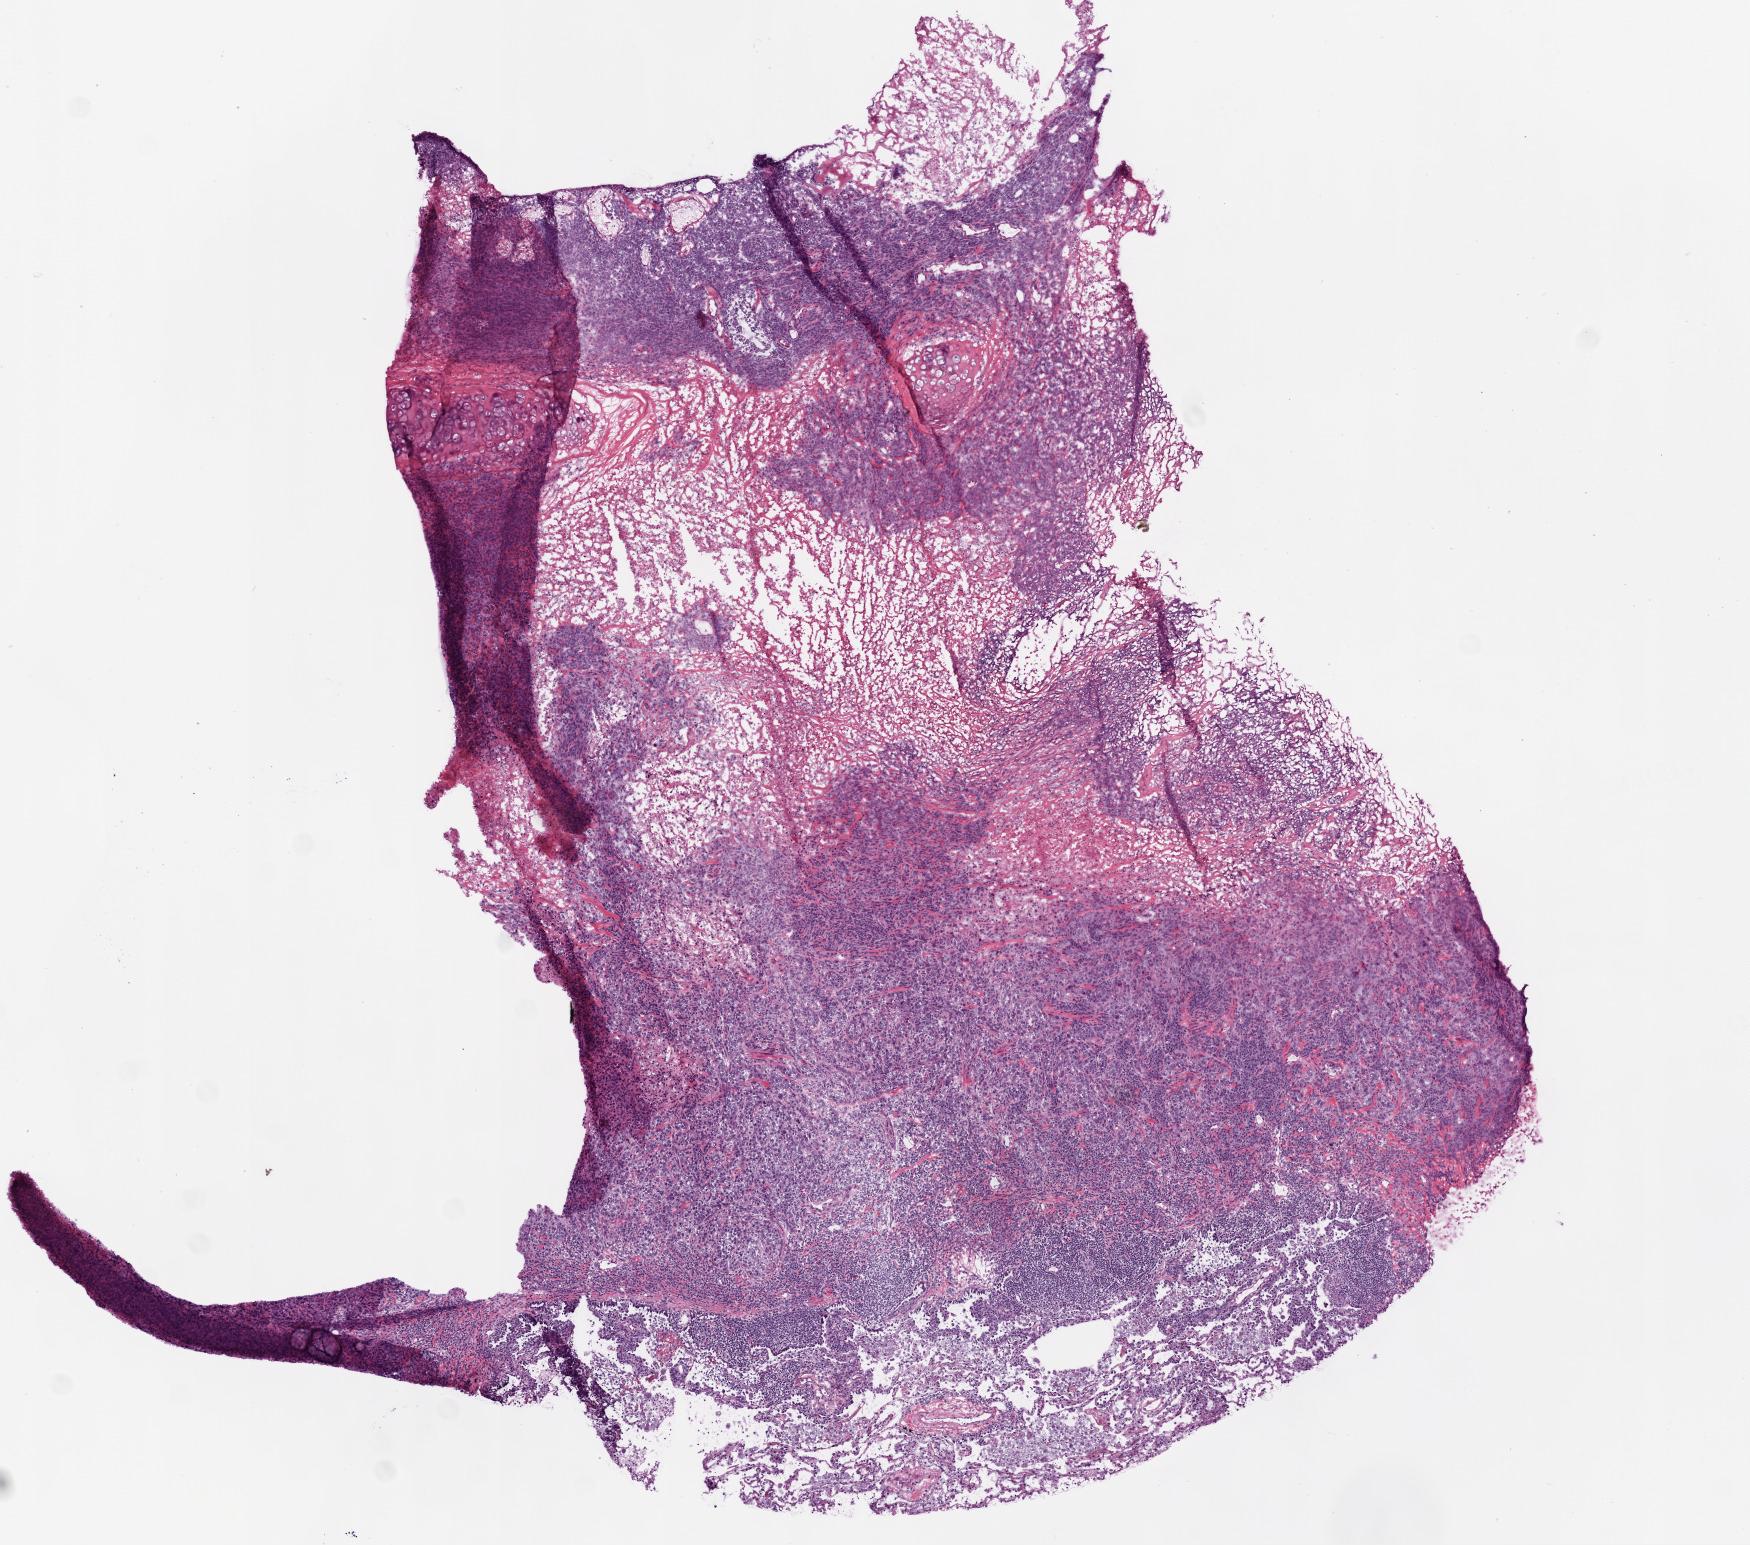
Whole-slide histology image, H&E, shown as a low-resolution overview of the whole scanned area (about 7.0 x 6.2 mm, from a 20x scan). Frozen section from the top of the tissue portion. Sample: primary tumour, lung. Male, age 71 years at initial diagnosis.
Histologic diagnosis: Squamous cell carcinoma, NOS (lower lobe, lung).